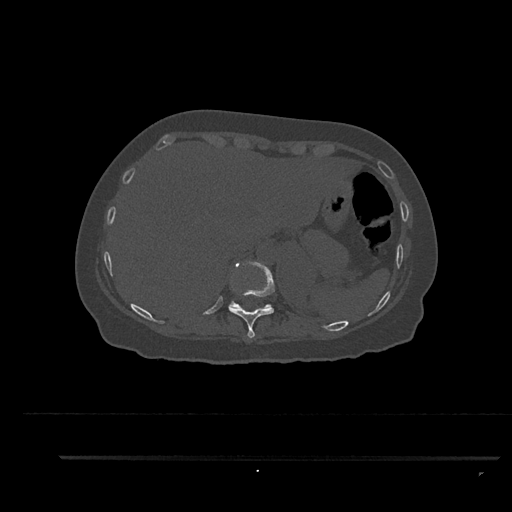
CT including the spine, one axial slice; slice 350 of 797 in the series (ordered by position); 120 kVp; bone window (W 1800 / L 400 HU); 512 × 512 image matrix, field of view 408 × 408 mm. Patient: female, 44 years. From the clinical record (not read from this slice): primary cancer: renal.
Annotated regions visible in this slice (semi-automatic segmentation, software-assisted and operator-edited):
- T10 vertebra: bounding box <229,260,275,338> (left, top, right, bottom; pixels)
- T11 vertebra: <228,300,271,307>